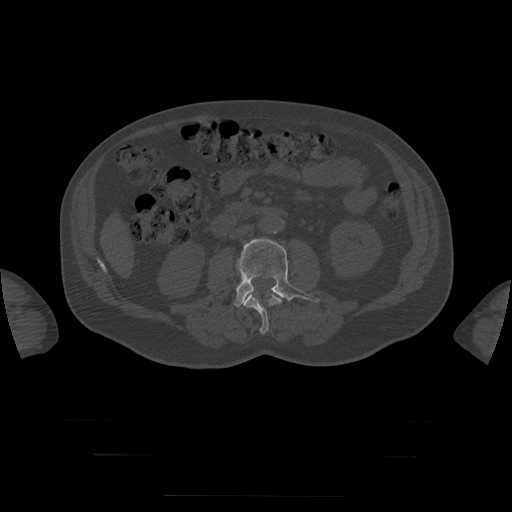
CT including the spine, one axial slice. Slice 5 of 397 in the series (ordered by position). Reconstruction kernel STANDARD. 120 kVp. Bone window (W 1800 / L 400 HU). 1.25 mm slice thickness. 512 × 512 image matrix, field of view 510 × 510 mm. Patient age 73 years. From the clinical record (not read from this slice): primary cancer: prostate.
Structures marked on this image (semi-automatically segmented with operator editing):
- L3 vertebra: bounding box (x1, y1, x2, y2) in pixels: (234, 239, 320, 307)